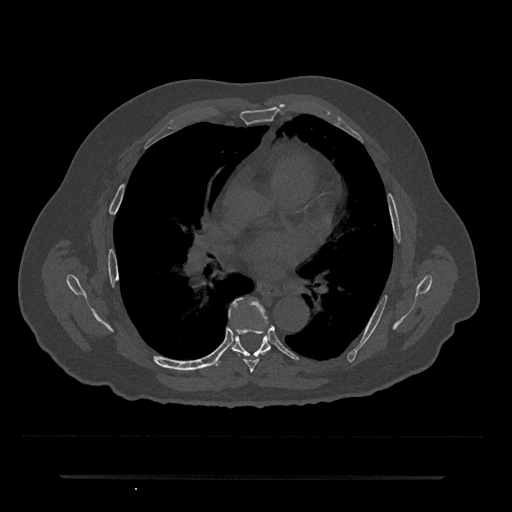
CT including the spine, one axial slice. Position 411 of 797 along the scan axis. Reconstruction kernel Br40s/3. Bone window (W 1800 / L 400 HU). 0.5 mm slice thickness. 512 × 512 image matrix, field of view 437 × 437 mm. Patient: male, 69 years. From the clinical record (not read from this slice): primary cancer: prostate.
Annotated regions visible in this slice (semi-automatically segmented with operator editing):
- T6 vertebra: box from (x=234, y=298) to (x=267, y=373) px
- T7 vertebra: (x=215, y=329)–(x=271, y=366)